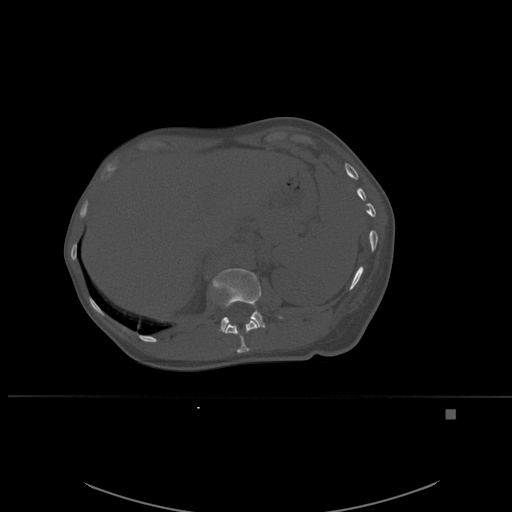
CT including the spine, one axial slice. Position 269 of 537 along the scan axis. Bone window (W 1800 / L 400 HU). 1.5 mm slice thickness. 512 × 512 image matrix. Patient: female, 45 years. From the clinical record (not read from this slice): primary cancer: lung.
Outlined on this slice (semi-automatic segmentation, software-assisted and operator-edited):
- L1 vertebra: bounding box (x1, y1, x2, y2) in pixels: (212, 268, 282, 333)
- T12 vertebra: (225, 320, 259, 353)